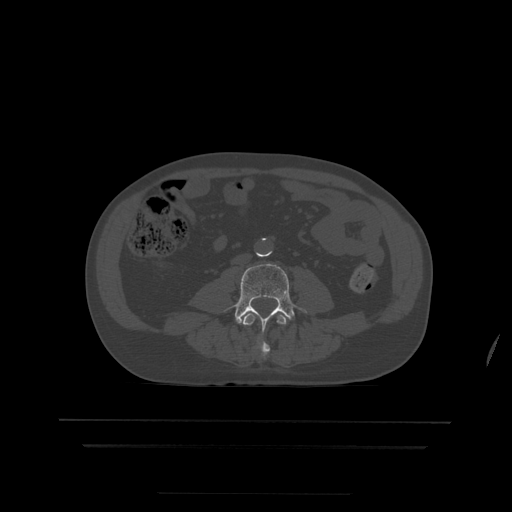
CT including the spine, one axial slice. Slice 101 of 522 in the series (ordered by position). Bone window (W 1800 / L 400 HU). 1.25 mm slice thickness. 512 × 512 image matrix, field of view 436 × 436 mm. Patient age 68 years. From the clinical record (not read from this slice): primary cancer: urothelial.
Outlined on this slice (semi-automatic segmentation, software-assisted and operator-edited):
- L3 vertebra: bounding box (x1, y1, x2, y2) in pixels: (241, 313, 287, 357)
- L4 vertebra: (235, 263, 307, 332)